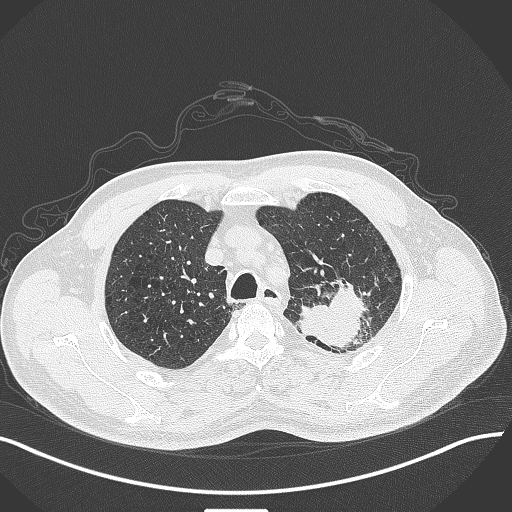
Chest CT, one axial slice. Position 335 of 429 along the scan axis. Reconstruction kernel B70f. Lung window (W 1500 / L -600 HU). 1 mm slice thickness. 512 × 512 image matrix. Patient: male, 55 years. From the clinical record (not read from this slice): clinical TNM (as recorded): T3 N0 M1c.
Annotated regions visible in this slice (rectangle marked by the reading radiologist):
- lung tumour (recorded histology: adenocarcinoma): box from (x=294, y=275) to (x=365, y=352) px